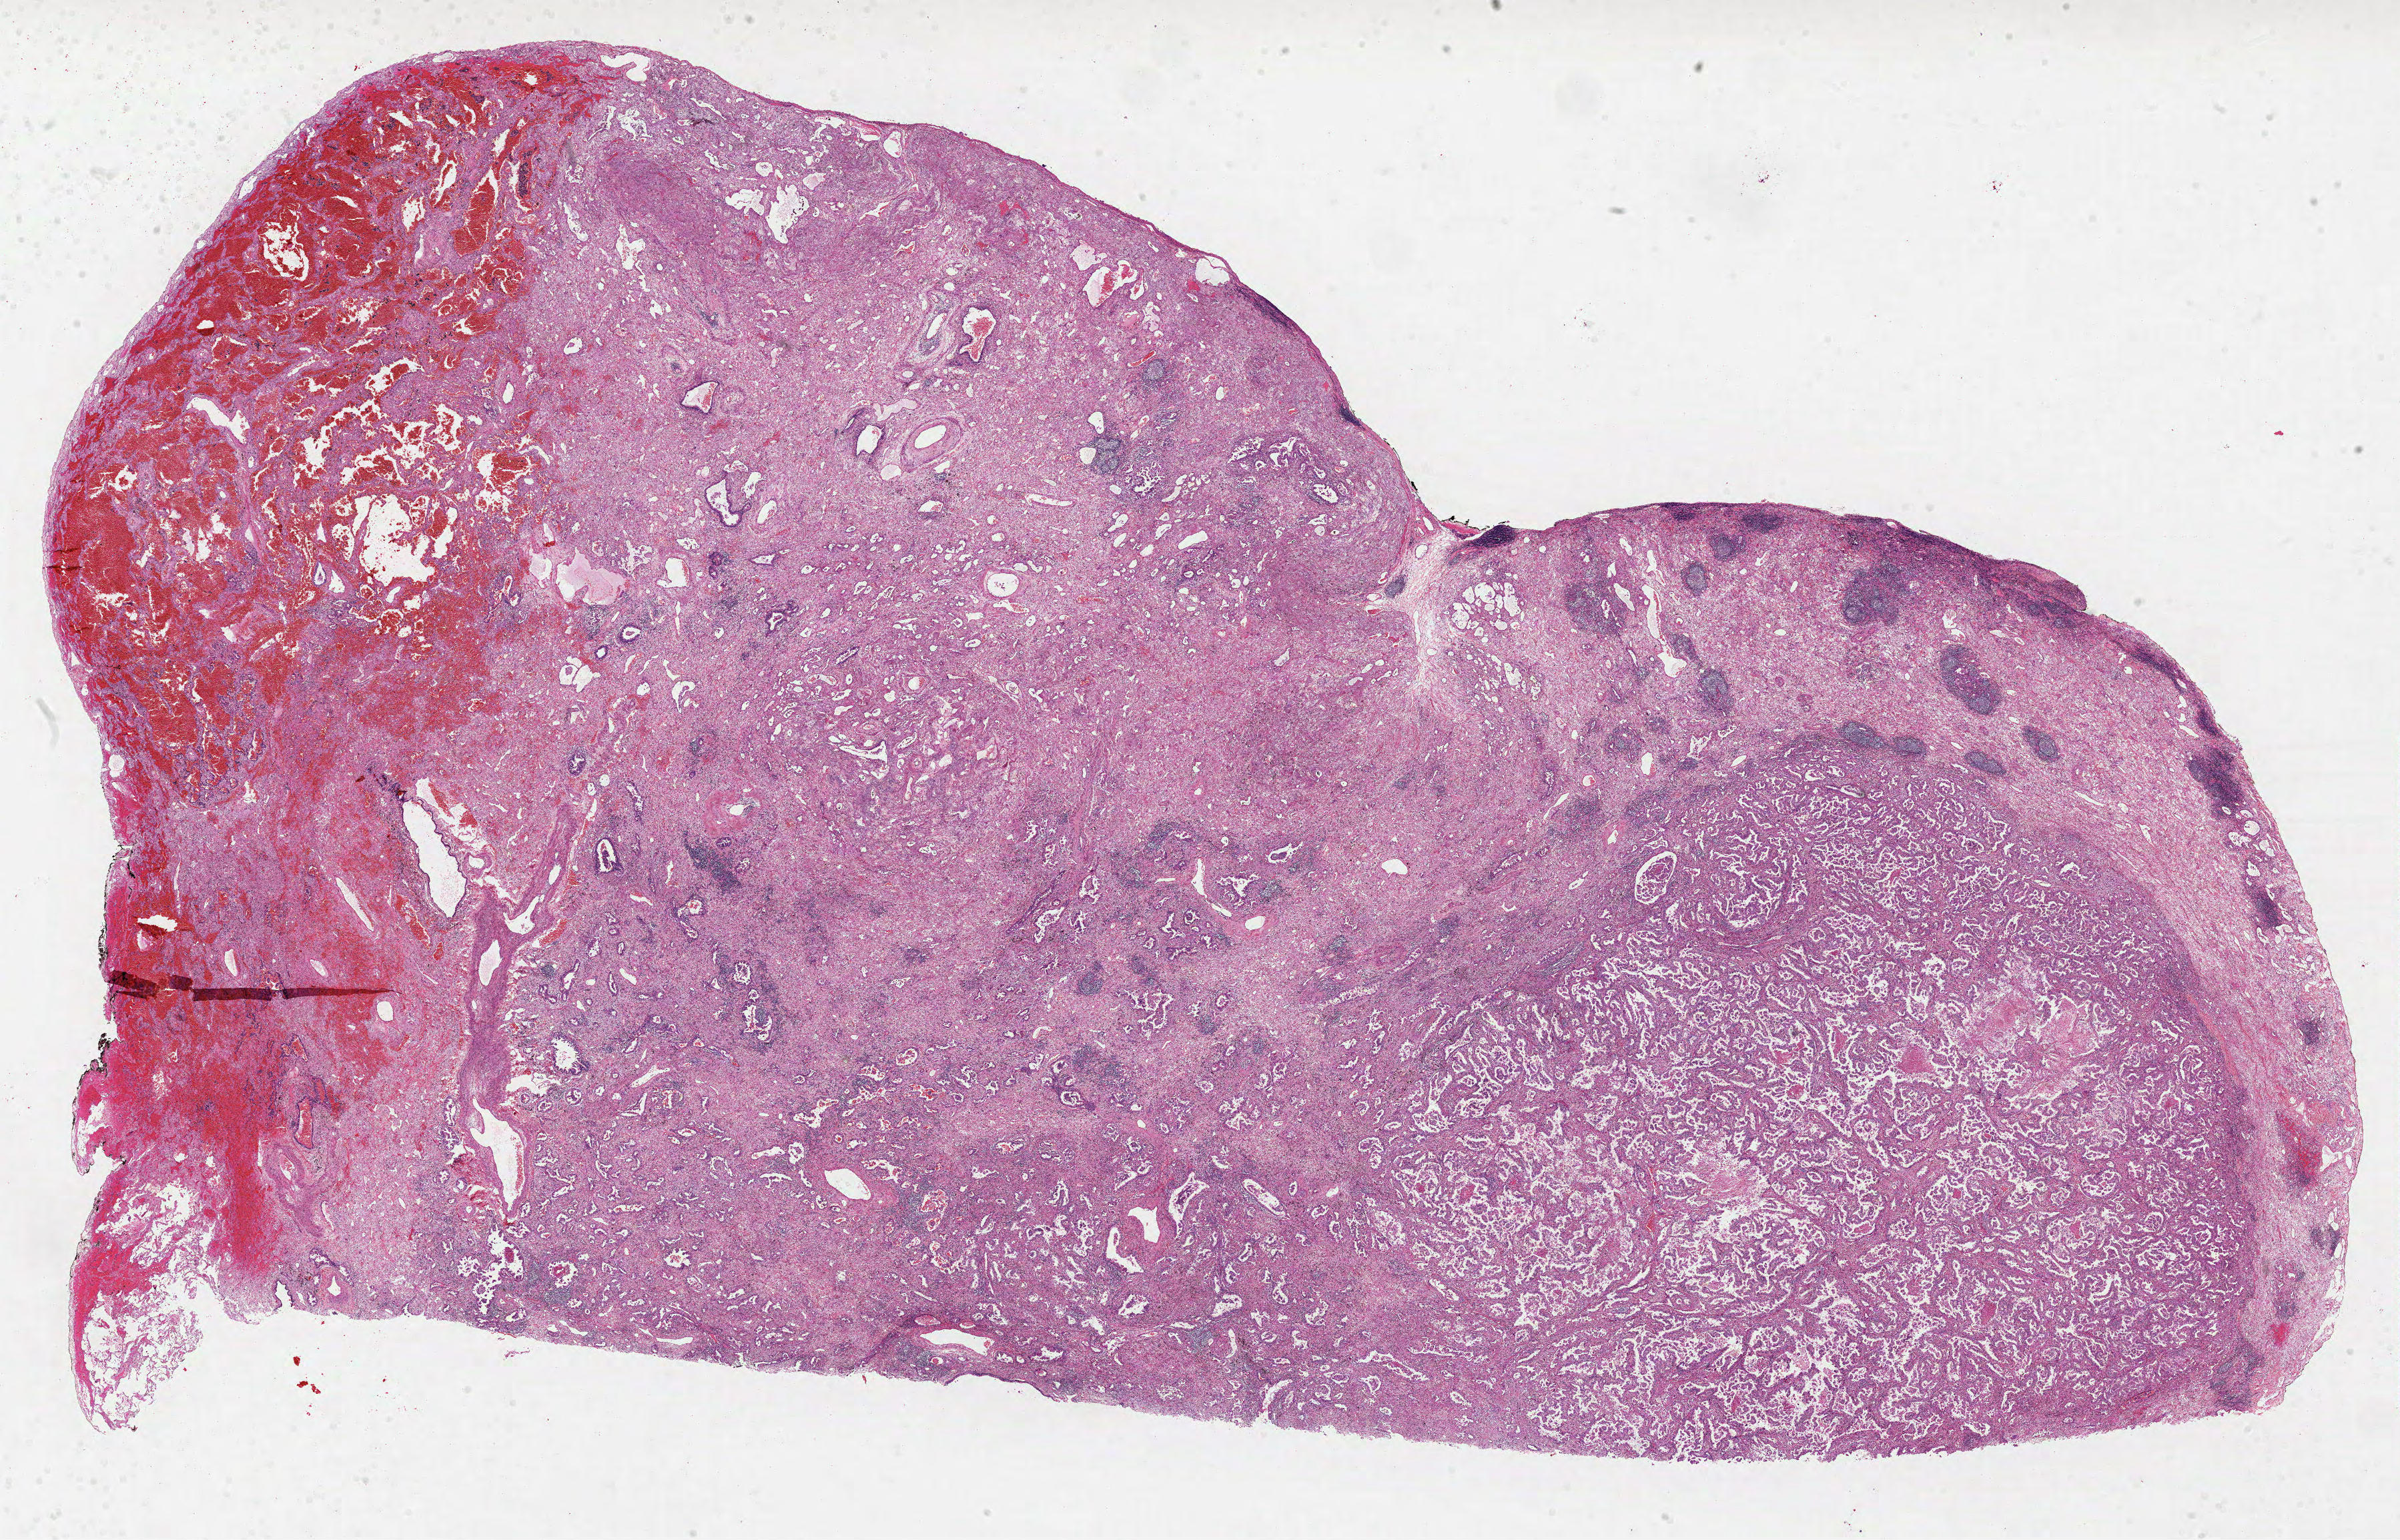
Digitized H&E tissue section (whole slide) — whole scanned area (about 29.0 x 18.6 mm) shown as a low-resolution overview, formalin-fixed paraffin-embedded (FFPE) diagnostic section, sample: primary tumour, lung. Patient: female, age at initial diagnosis 75 years.
• laterality: right
• pathologic diagnosis: Adenocarcinoma with mixed subtypes (upper lobe, lung)
• AJCC pathologic stage: IIA